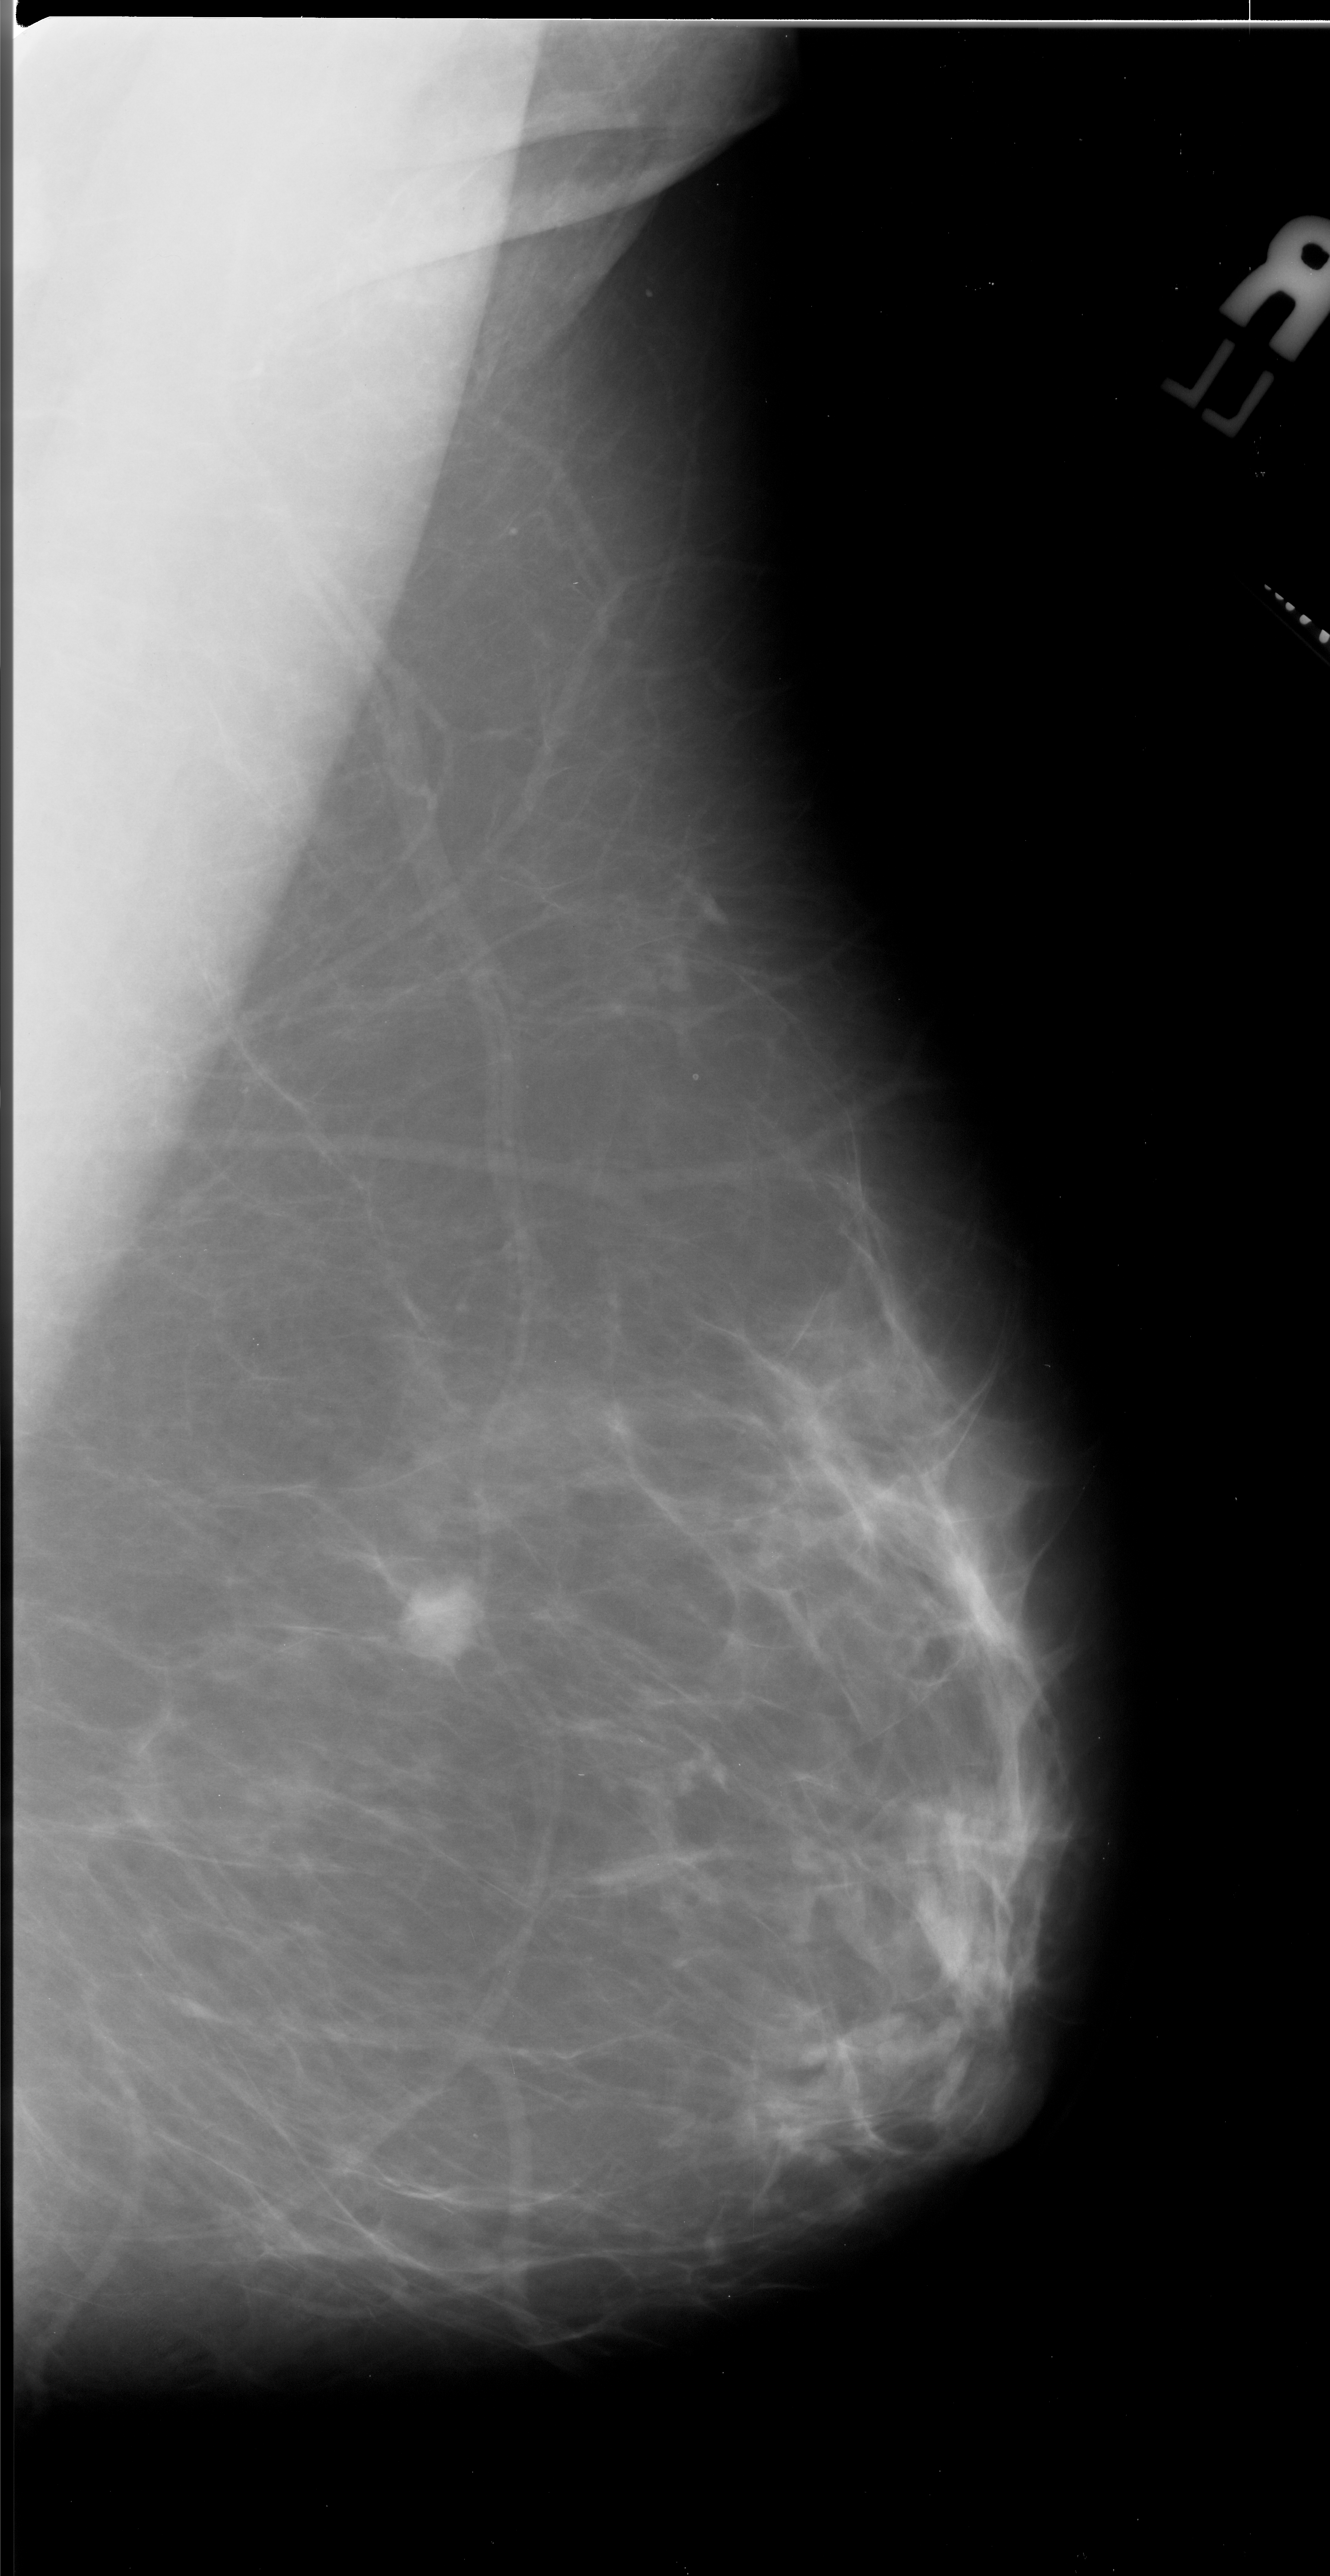
Scanned film-screen mammogram; right breast; mediolateral oblique (MLO) view; BI-RADS breast density category 2 (scale 1–4); 1330 × 2576 image matrix.
Expert-marked regions of interest on this image (one box per marked abnormality):
- mass, shape round, margins ill defined; BI-RADS assessment category 4; subtlety rating 4 on a 1 (subtle) to 5 (obvious) scale; pathology (as recorded): malignant: bounding box (x1, y1, x2, y2) in pixels: (392, 1572, 479, 1651)